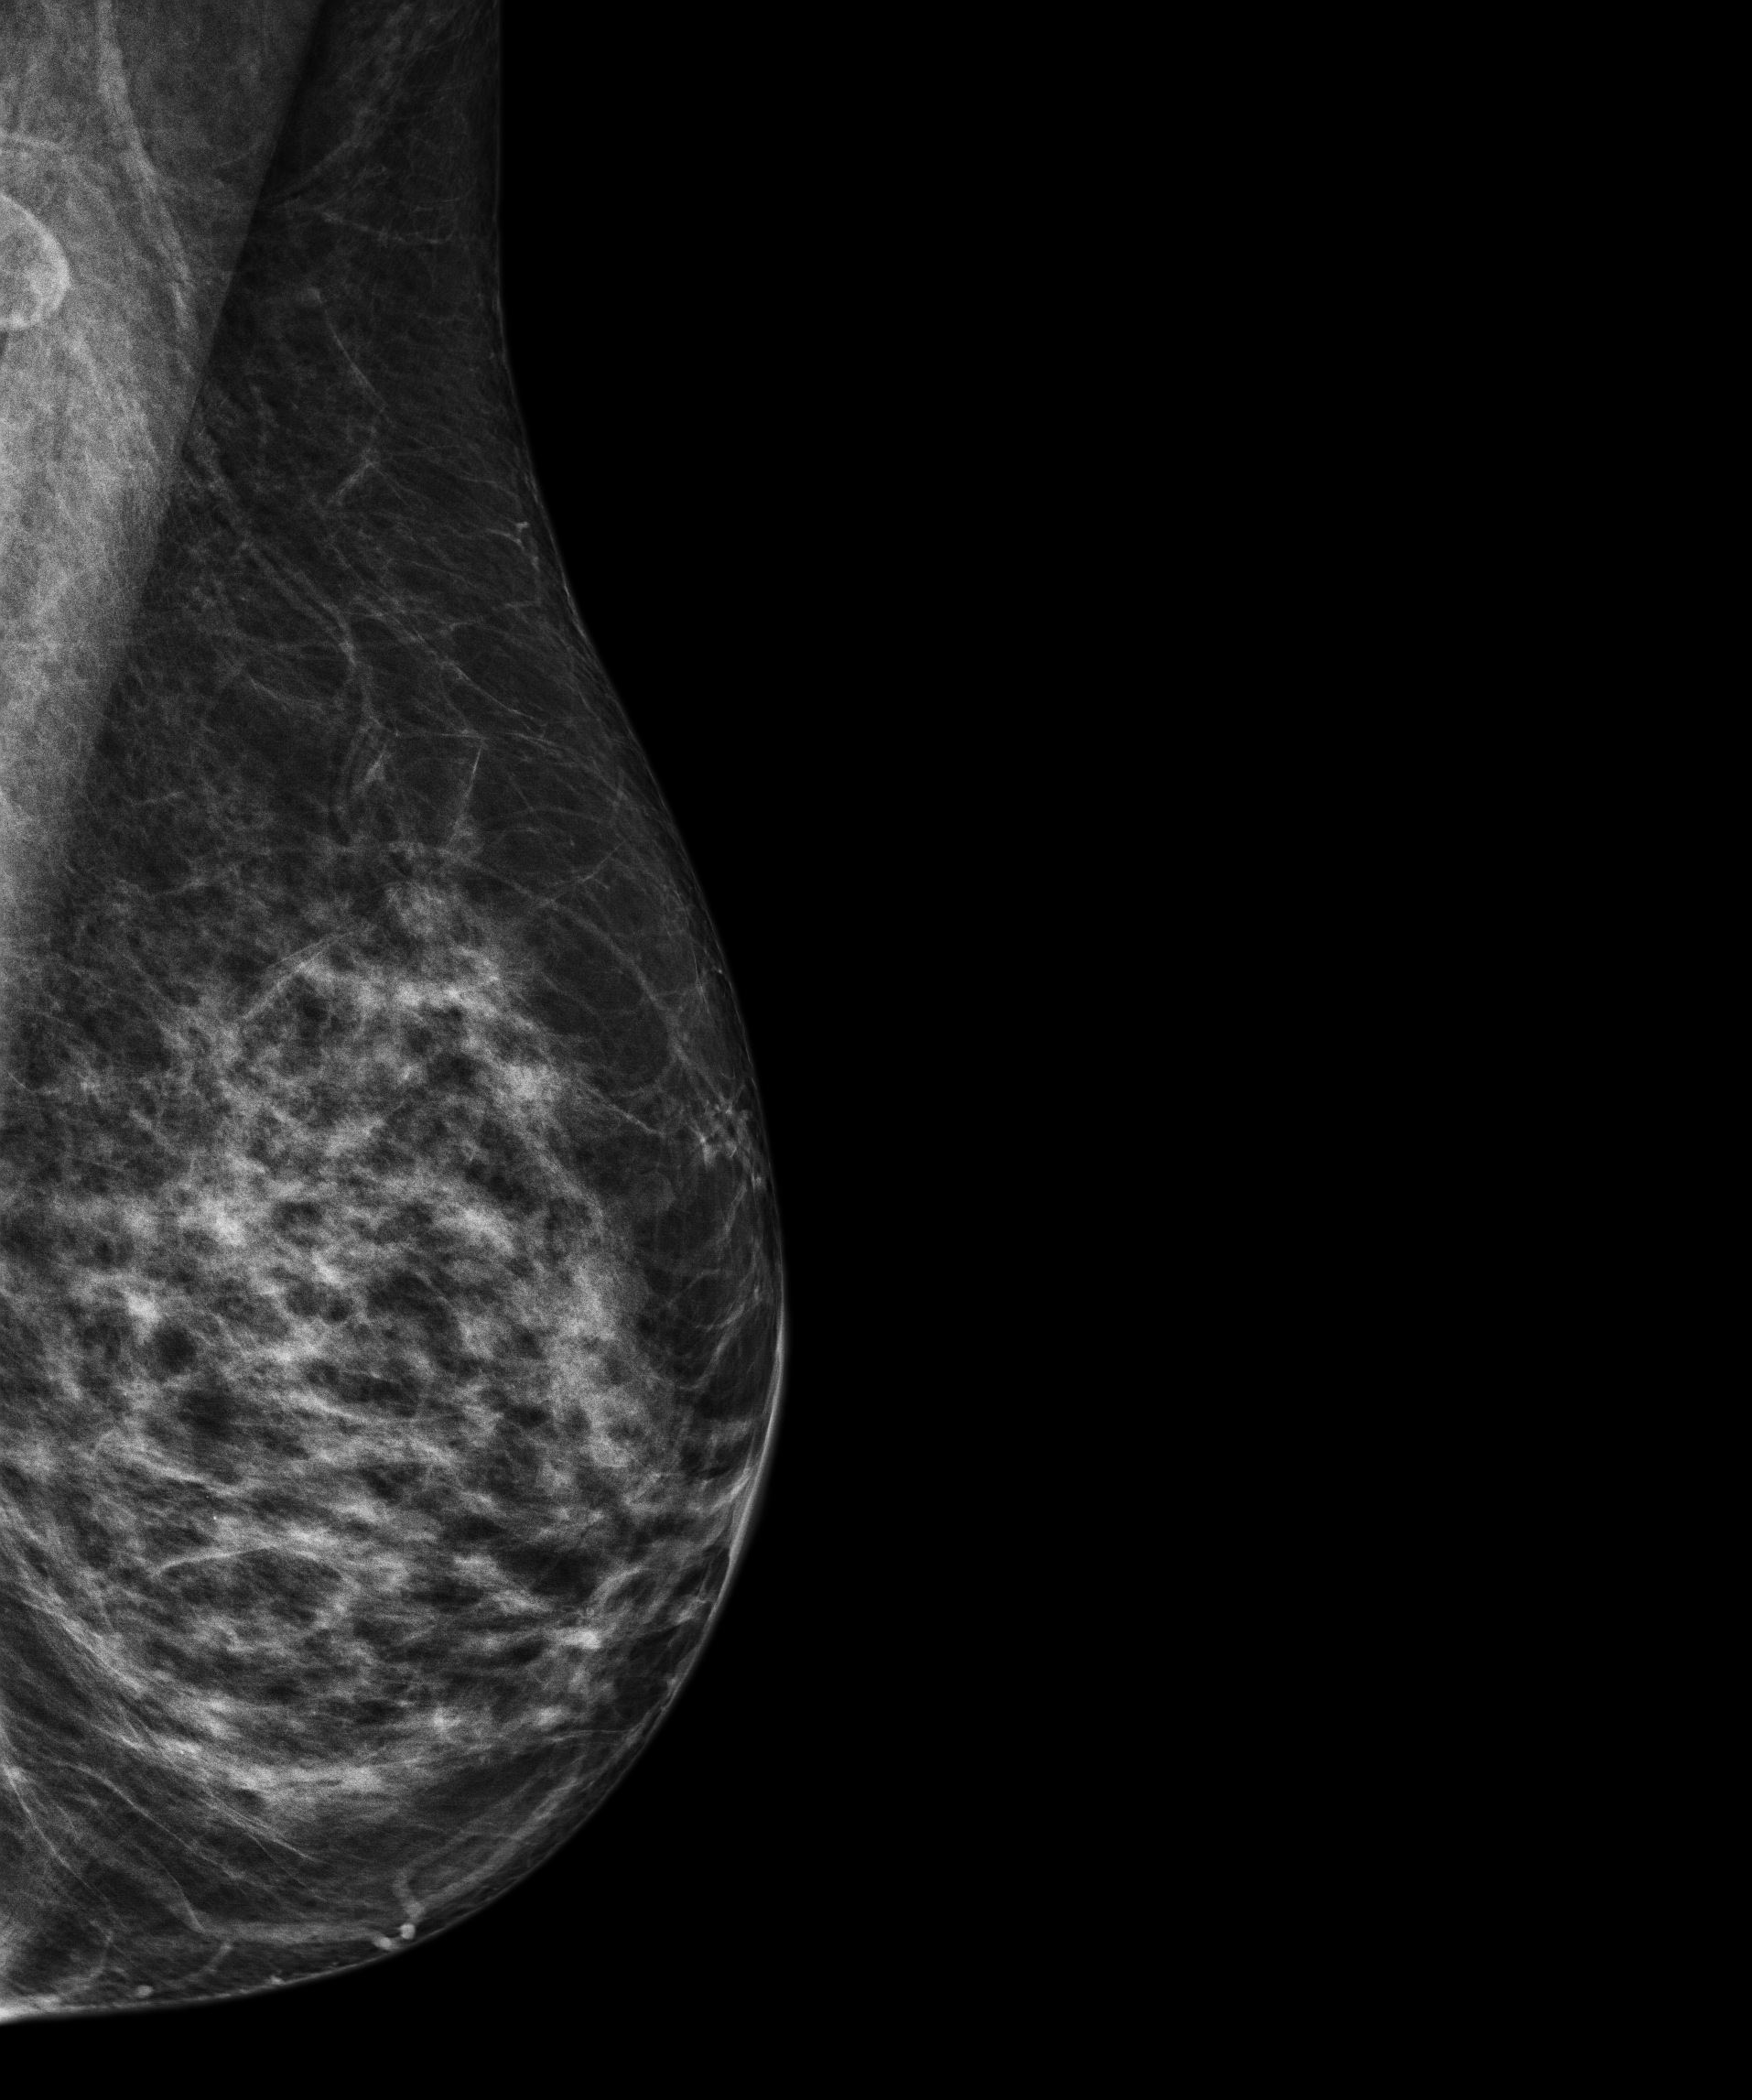
Annual screening mammography examination. Female patient, age 59 years.
Image type: full-field digital mammogram. Breast: left. Projection: medio-lateral oblique projection.